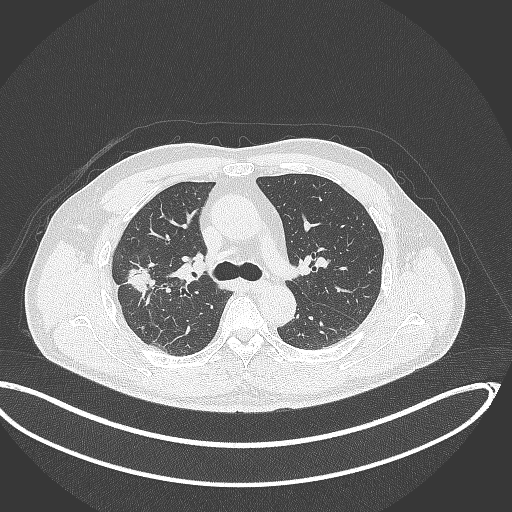
Chest CT, one axial slice. Position 224 of 391 along the scan axis. 120 kVp. Lung window (W 1500 / L -600 HU). 512 × 512 image matrix. Patient: male, 63 years. From the clinical record (not read from this slice): clinical TNM (as recorded): T1c N0 M0; histopathological grade: G2-3.
Outlined on this slice (bounding box drawn by a radiologist):
- lung tumour (recorded histology: adenocarcinoma): box from (x=118, y=257) to (x=165, y=302) px